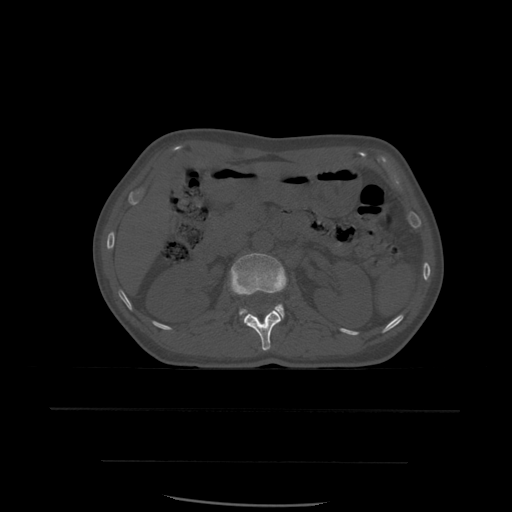
CT including the spine, one axial slice; slice 238 of 574 in the series (ordered by position); bone window (W 1800 / L 400 HU); 512 × 512 image matrix, field of view 392 × 392 mm. Patient age 48 years. Case-level facts recorded for this patient, not image findings: primary cancer: lung.
Outlined on this slice (semi-automatically segmented with operator editing):
- L1 vertebra: box from (x=244, y=310) to (x=282, y=351) px
- L2 vertebra: (x=229, y=253)–(x=287, y=321)